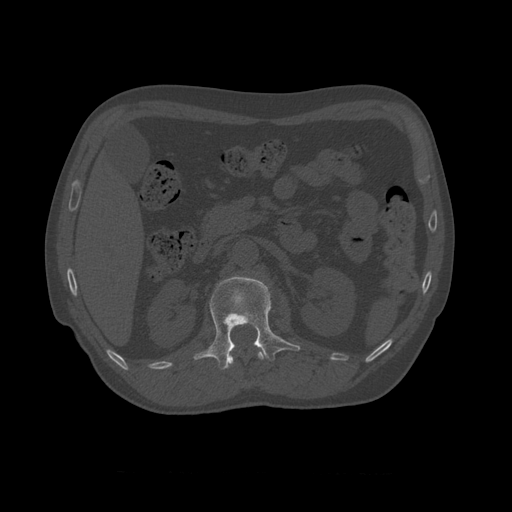
CT including the spine, one axial slice; slice 357 of 450 in the series (ordered by position); reconstruction kernel STANDARD; 120 kVp; bone window (W 1800 / L 400 HU); 1.25 mm slice thickness; 512 × 512 image matrix, field of view 405 × 405 mm. Patient age 75 years. Case-level facts recorded for this patient, not image findings: primary cancer: prostate.
Annotated regions visible in this slice (semi-automatic segmentation, software-assisted and operator-edited):
- L1 vertebra: bounding box (x1, y1, x2, y2) in pixels: (194, 275, 301, 370)
- T10 vertebra: (224, 343, 264, 369)
- T11 vertebra: (226, 353, 264, 369)